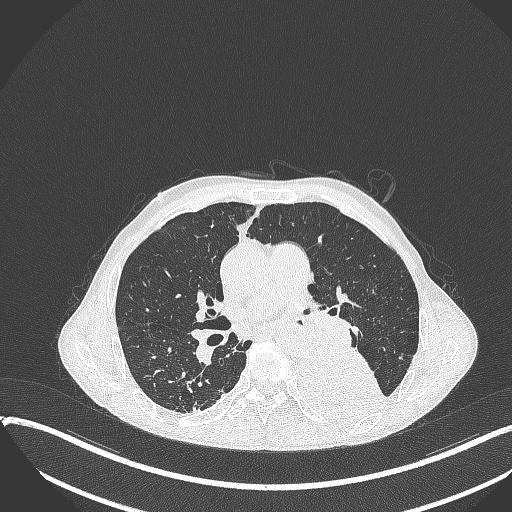
Chest CT, one axial slice. Slice 208 of 401 in the series (ordered by position). Reconstruction kernel B70f. 120 kVp. Lung window (W 1500 / L -600 HU). 1 mm slice thickness. 512 × 512 image matrix, field of view 400 × 400 mm. Male patient, age 57 years. From the clinical record (not read from this slice): clinical TNM (as recorded): T4 N0 M0.
Structures marked on this image (bounding box drawn by a radiologist):
- lung tumour (recorded histology: squamous cell carcinoma): box from (x=294, y=348) to (x=393, y=420) px